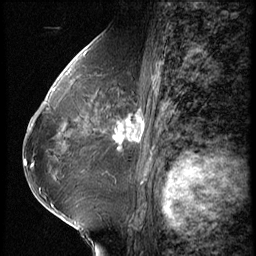
Breast MRI (dynamic contrast-enhanced), one sagittal slice. Position 31 of 62 along the scan axis. 3 images stored at this slice position (order not interpretable as contrast timing). 1.5 T. TE 4.2 ms, TR 9 ms. 256 × 256 image matrix, field of view 180 × 180 mm. Female patient, age 65 years. From the clinical record (not read from this slice): setting: breast cancer imaged before/during neoadjuvant chemotherapy; receptor status: HR-positive, HER2-negative.
Structures marked on this image (semi-automatic segmentation, software-assisted and operator-edited):
- analysis volume of interest (the breast-tissue region the enhancement analysis was run in; not a lesion): bounding box <104,104,154,161> (left, top, right, bottom; pixels)
- tumour enhancement mask (voxels above the 140 % enhancement threshold inside the analysis volume of interest): <114,110,144,149>